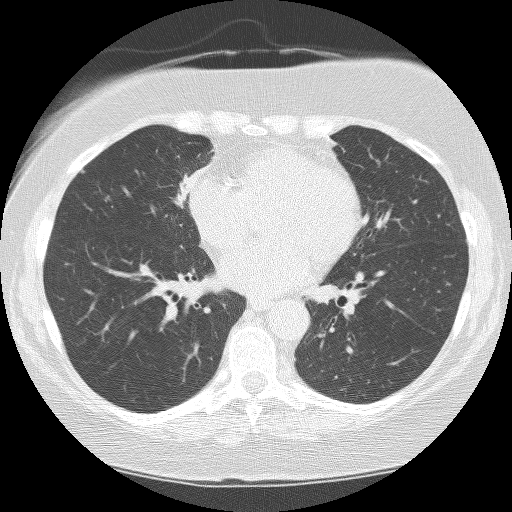
Low-dose screening chest CT, one axial slice; slice 79 of 159 in the series (ordered by position); reconstruction kernel BONE; 120 kVp; lung window (W 1500 / L -600 HU); 2.5 mm slice thickness; 512 × 512 image matrix, field of view 299 × 299 mm.
Annotated regions visible in this slice (manually delineated by an expert):
- lesion 1 (tumor, hilum of right lung): bounding box [x1, y1, x2, y2] px = [175, 164, 212, 209]